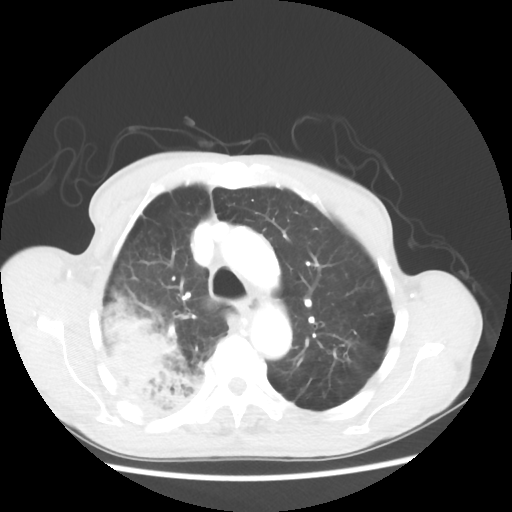
Chest CT, one axial slice; slice 40 of 58 in the series (ordered by position); reconstruction kernel STANDARD; 100 kVp; lung window (W 1500 / L -600 HU); 5 mm slice thickness; 512 × 512 image matrix, field of view 351 × 351 mm. Patient: male, 75 years. From the clinical record (not read from this slice): clinical TNM (as recorded): T4 N1 M1.
Structures marked on this image (bounding box drawn by a radiologist):
- lung tumour (recorded histology: adenocarcinoma): bounding box <96,288,208,411> (left, top, right, bottom; pixels)